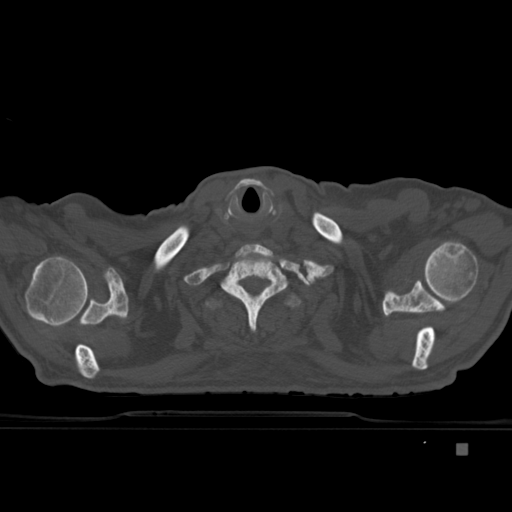
CT including the spine, one axial slice; slice 358 of 451 in the series (ordered by position); bone window (W 1800 / L 400 HU); 1.5 mm slice thickness; 512 × 512 image matrix, field of view 378 × 378 mm. Patient: male, 75 years. From the clinical record (not read from this slice): primary cancer: prostate.
Annotated regions visible in this slice (semi-automatic segmentation, software-assisted and operator-edited):
- T1 vertebra: bounding box <220,244,304,333> (left, top, right, bottom; pixels)
- T2 vertebra: <206,295,301,307>